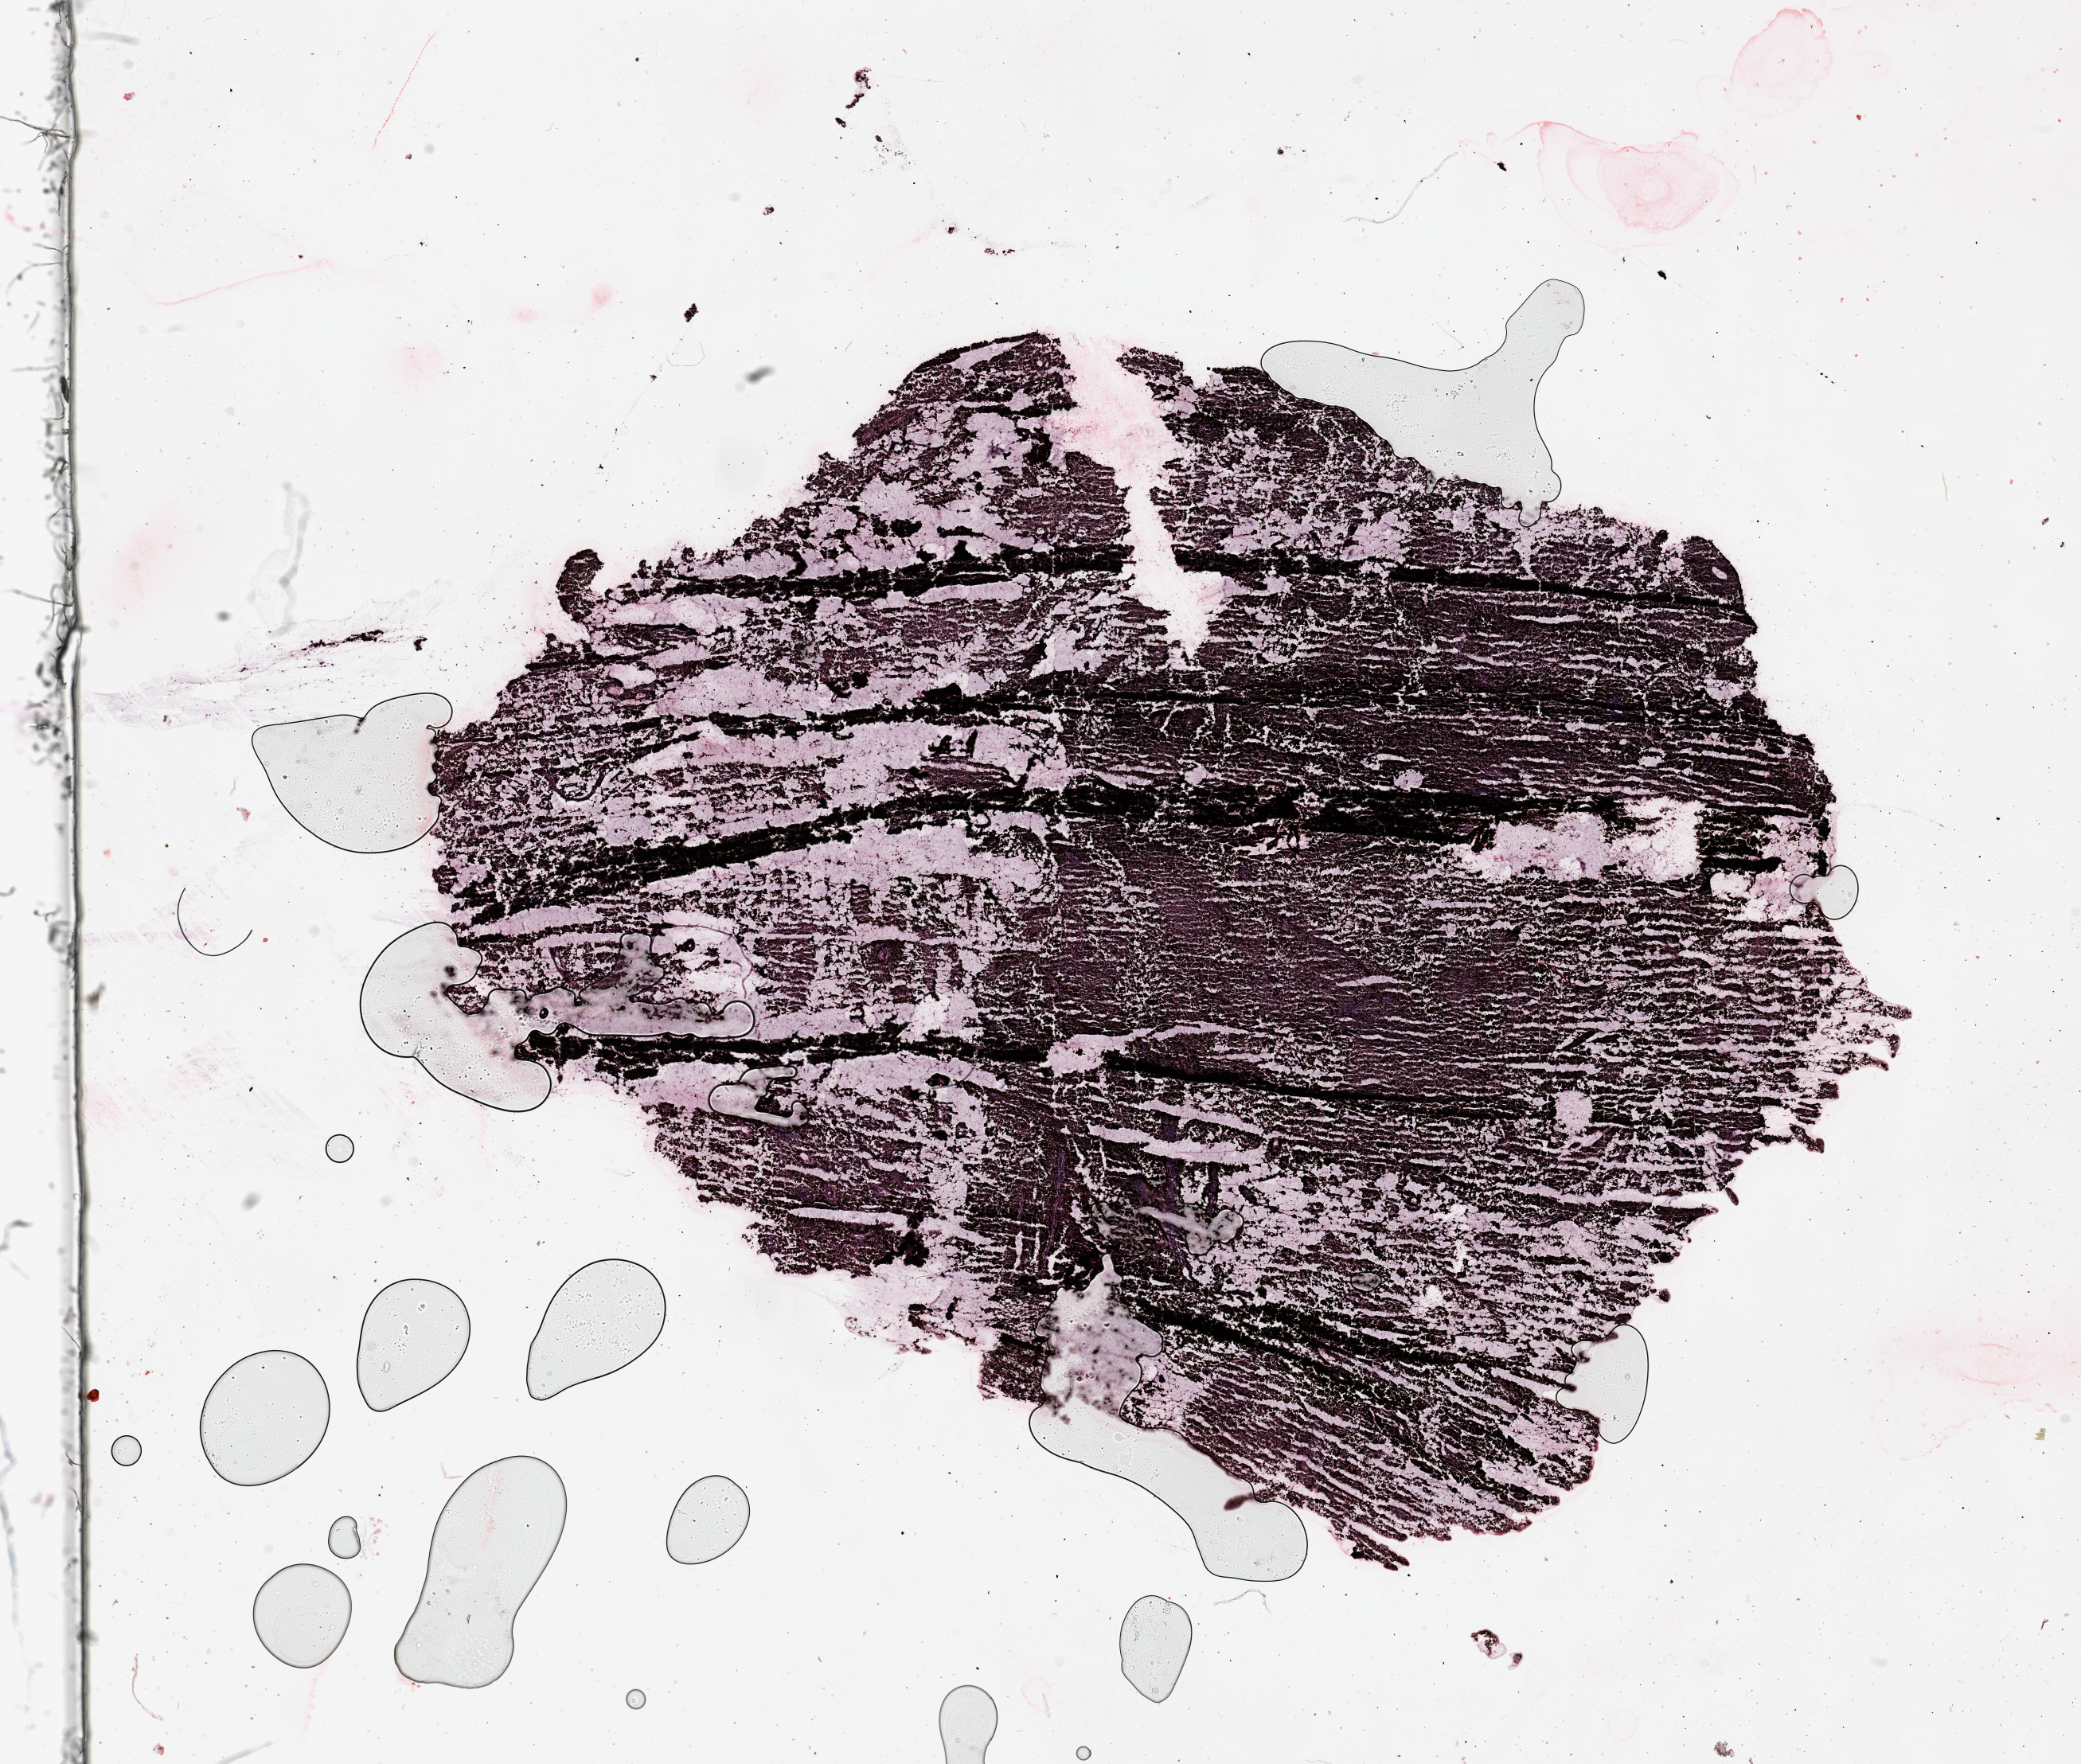
Whole-slide histology image, Hematoxylin and eosin (H&E) stained, shown as a low-resolution overview of the whole scanned area (about 20.7 x 17.5 mm, slide scanned at 20x); melanoma tumour tissue; sampled site not recorded. Female, 74 y/o.
Patient diagnosis (cohort enrolment): cutaneous melanoma (skin).